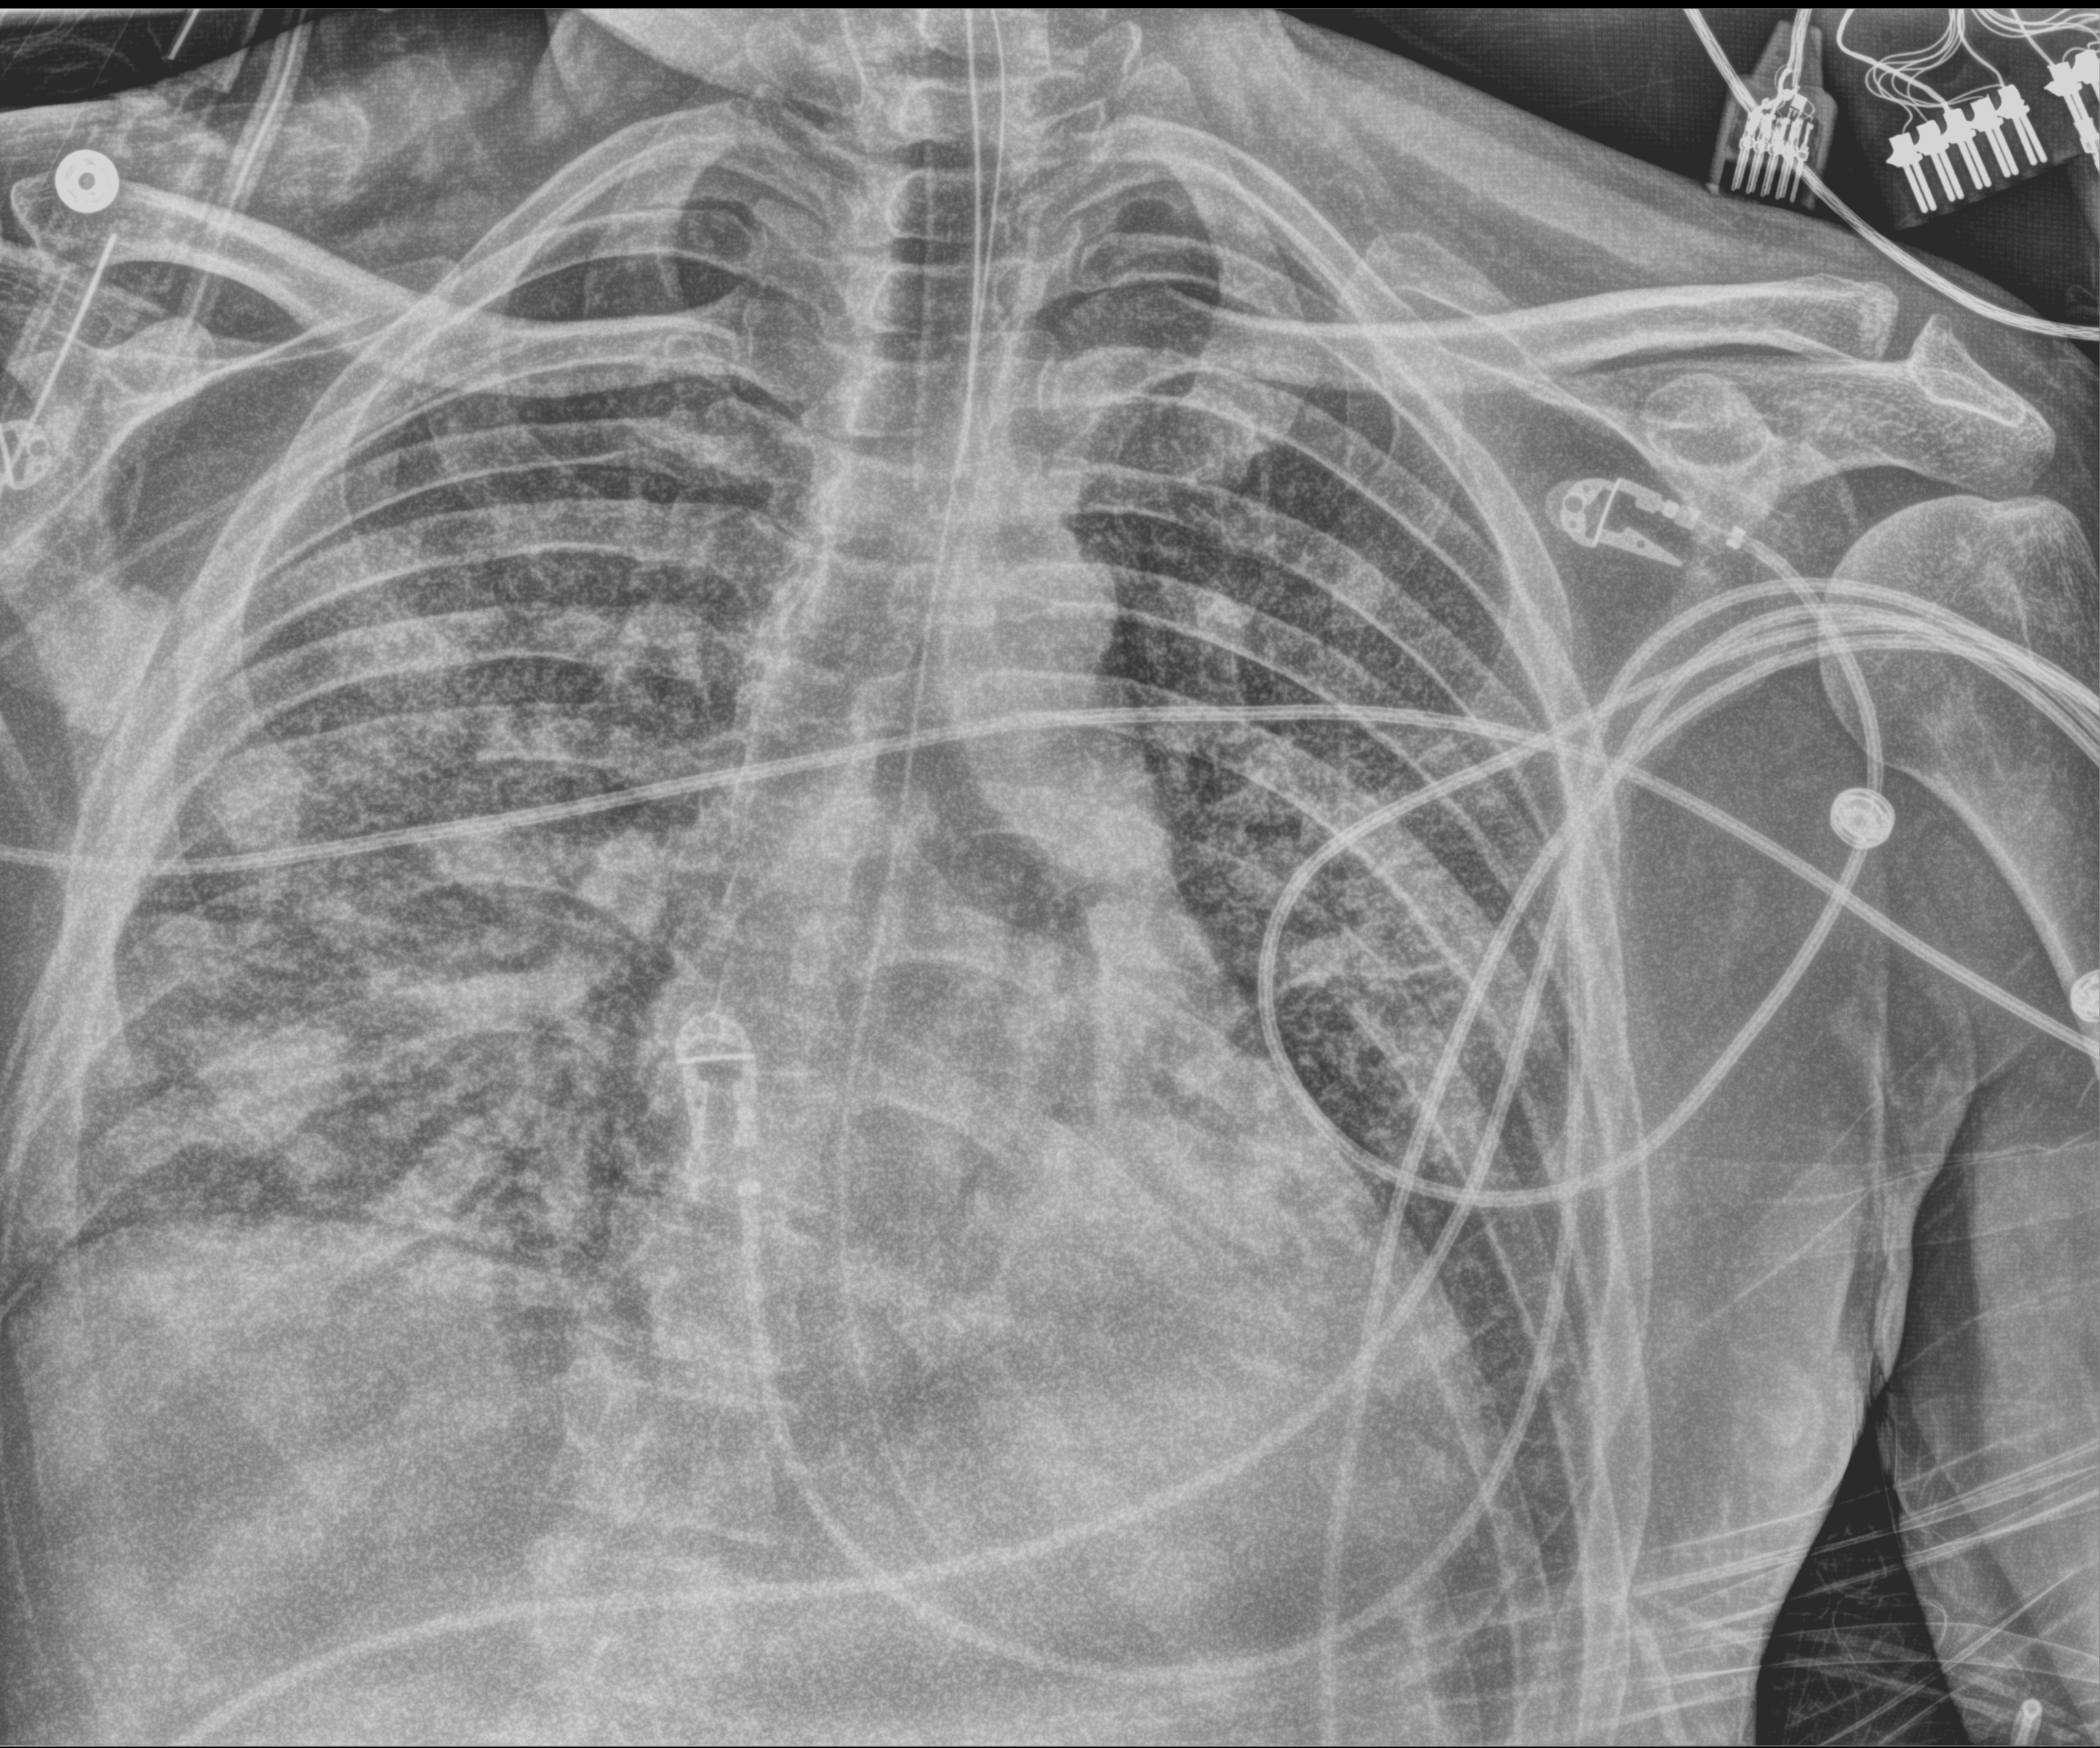
Chest X-ray (portable); anteroposterior (AP) projection. Patient hospitalised with COVID-19; male, aged 18–59 years.
Admission-level facts for this patient (not findings on this image; timing relative to this image not recorded):
- mechanically ventilated during this hospital stay: yes